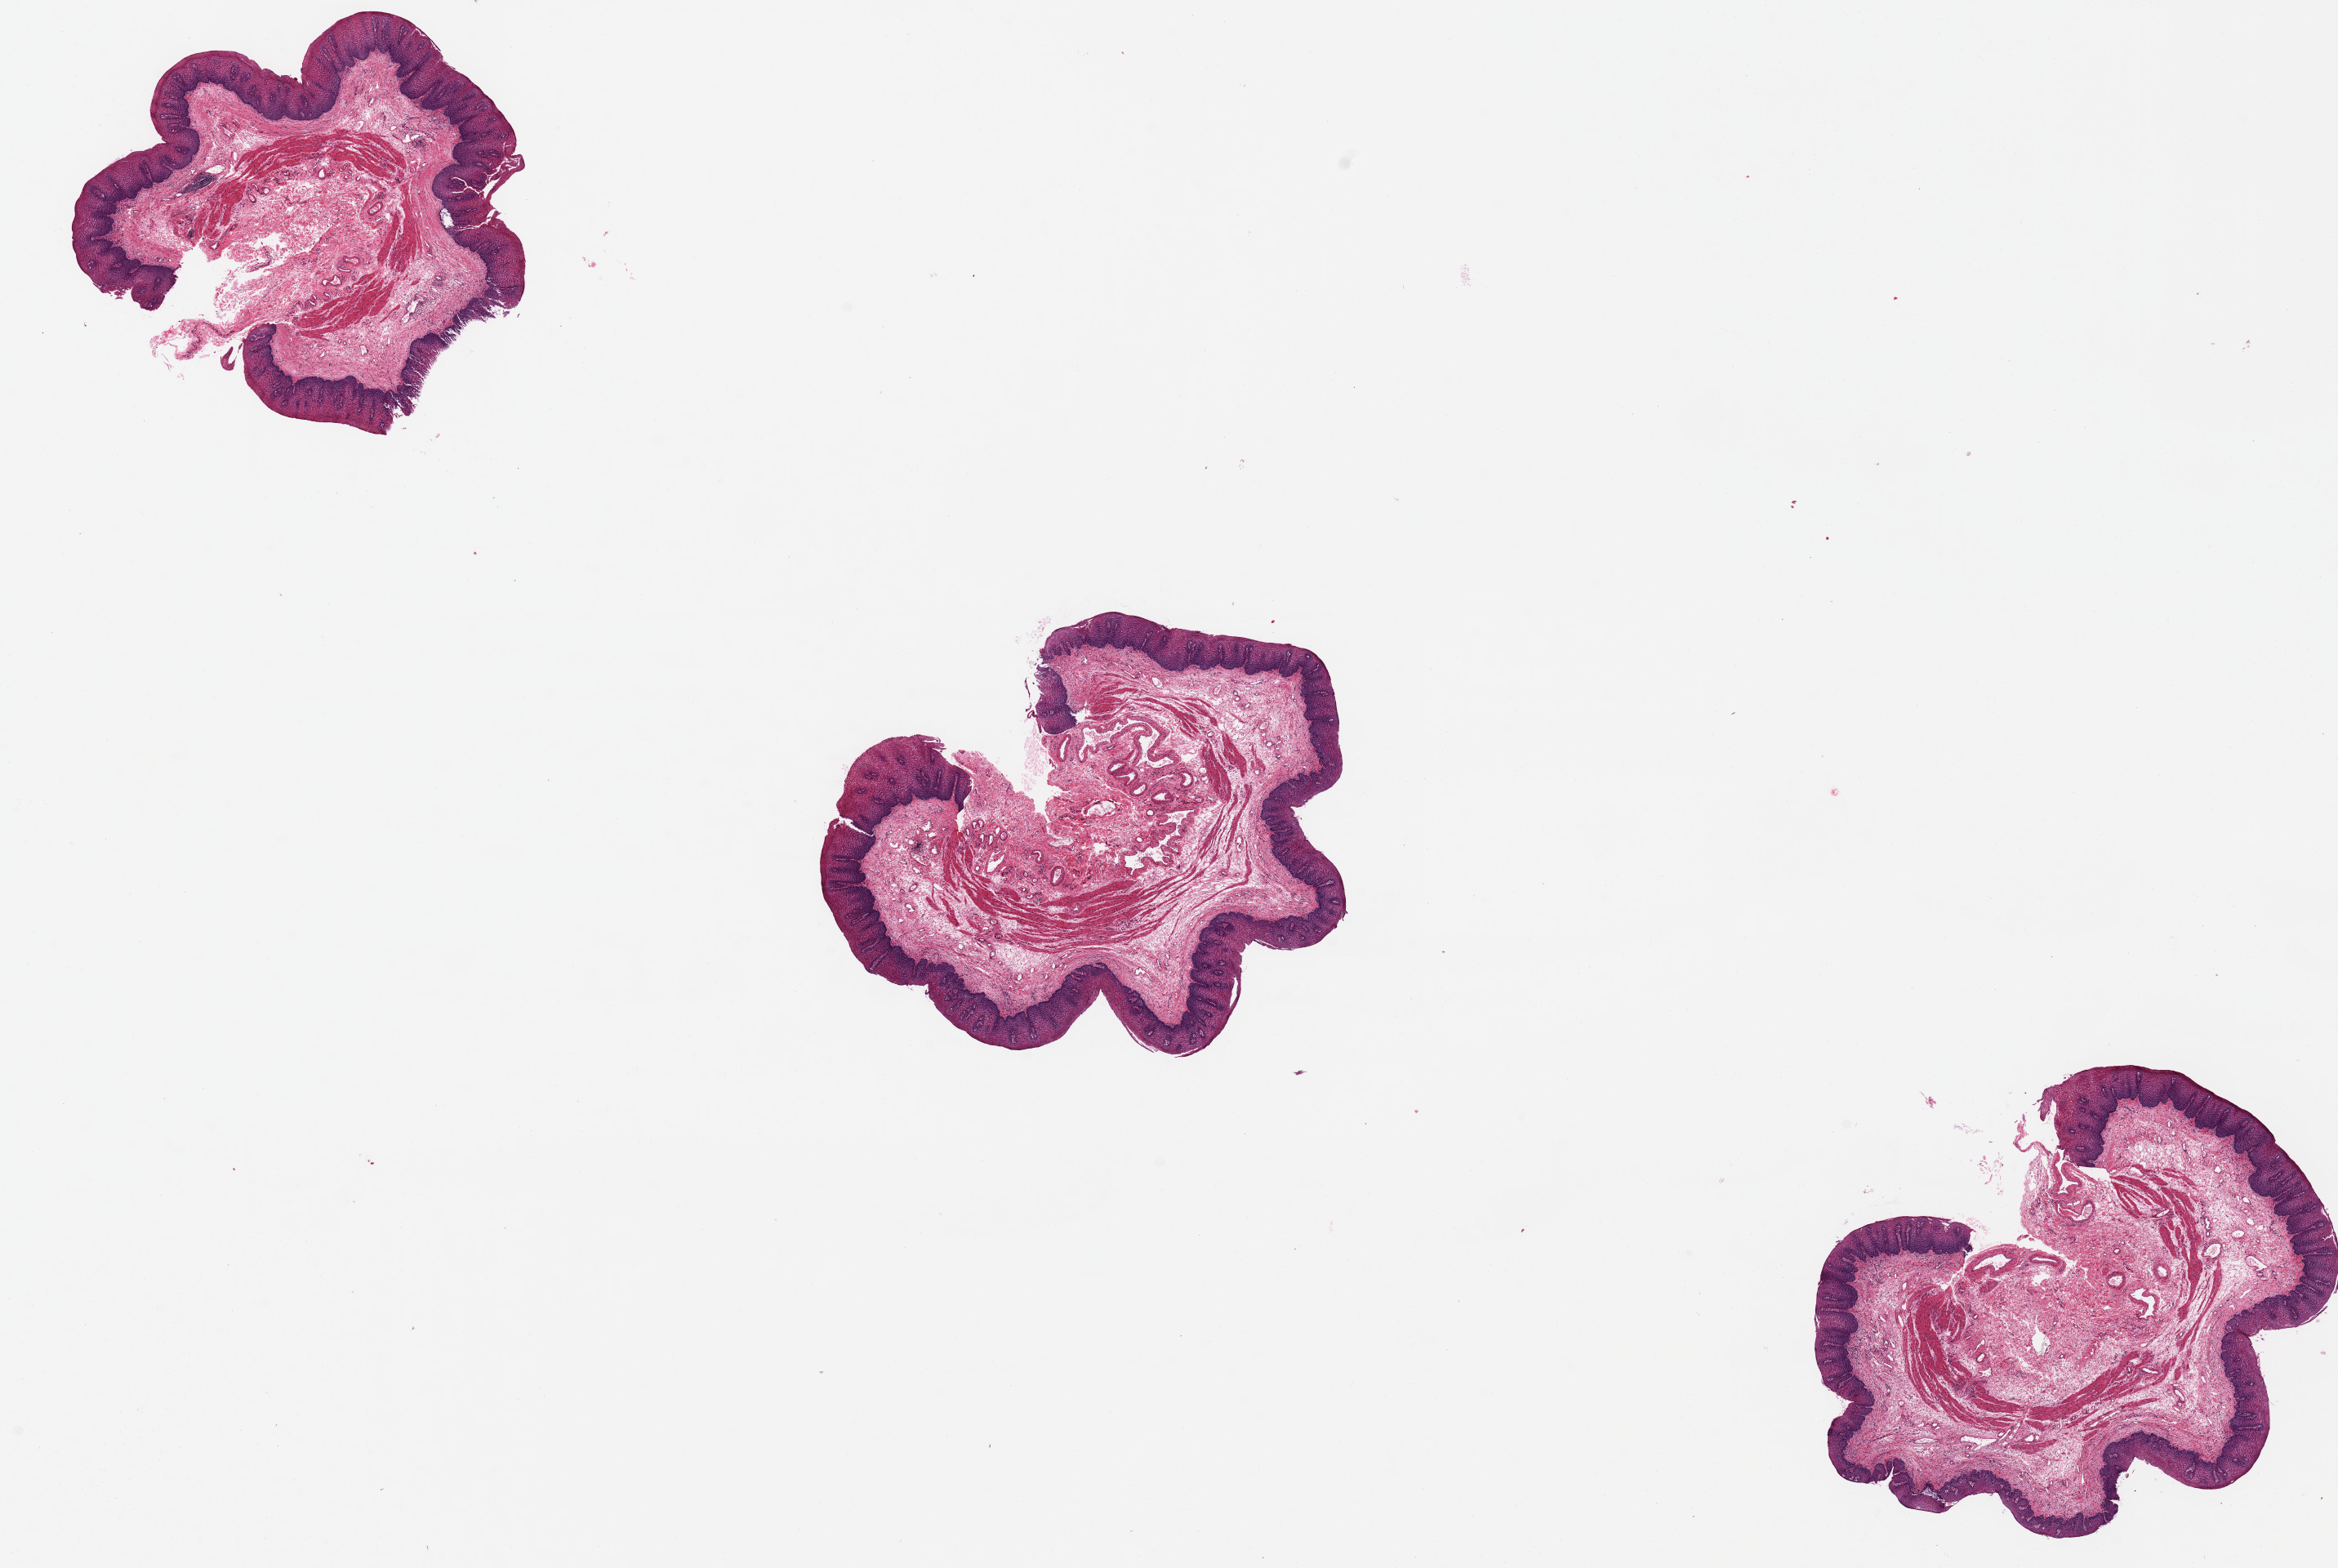
Digitized H&E-stained section — shown as a low-resolution overview of the whole scanned area (about 22.6 x 15.2 mm, from a 20x scan), PAXgene-fixed, paraffin-embedded tissue, sampled site (target tissue): esophageal muscle, tissue donor sample. Female donor.
* reviewer comment on this tissue sample: 3 pieces